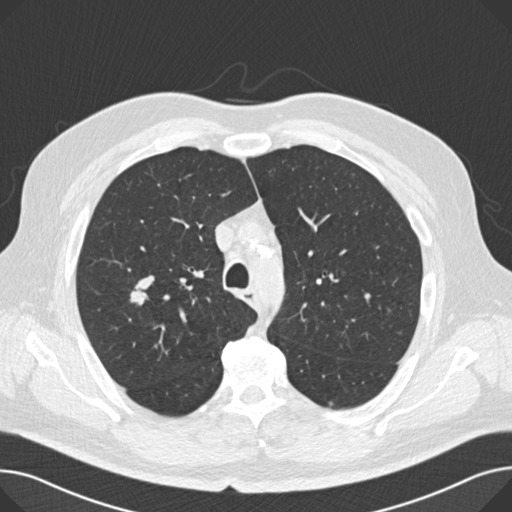
Axial slice from a low-dose chest CT screening exam. Second screening round (one year after baseline). Lung window (W 1500 / L -600 HU). Standard (soft-tissue) reconstruction kernel (B30f). Slice 47 of 166 in the series. 512 × 512 image matrix, field of view 374 × 374 mm. Male, age 67 years at enrolment. Current smoker at enrolment.
- Lesion marked by an expert reader, bounding box [x1, y1, x2, y2] px = [120, 272, 164, 312].
- Screening reader's record for this exam: no non-calcified nodule ≥4 mm recorded.
- Participant outcome: lung cancer diagnosed 194 days after this screen — small cell carcinoma, NOS, right middle lobe, stage IA (AJCC 6th edition), 20 mm at pathology.